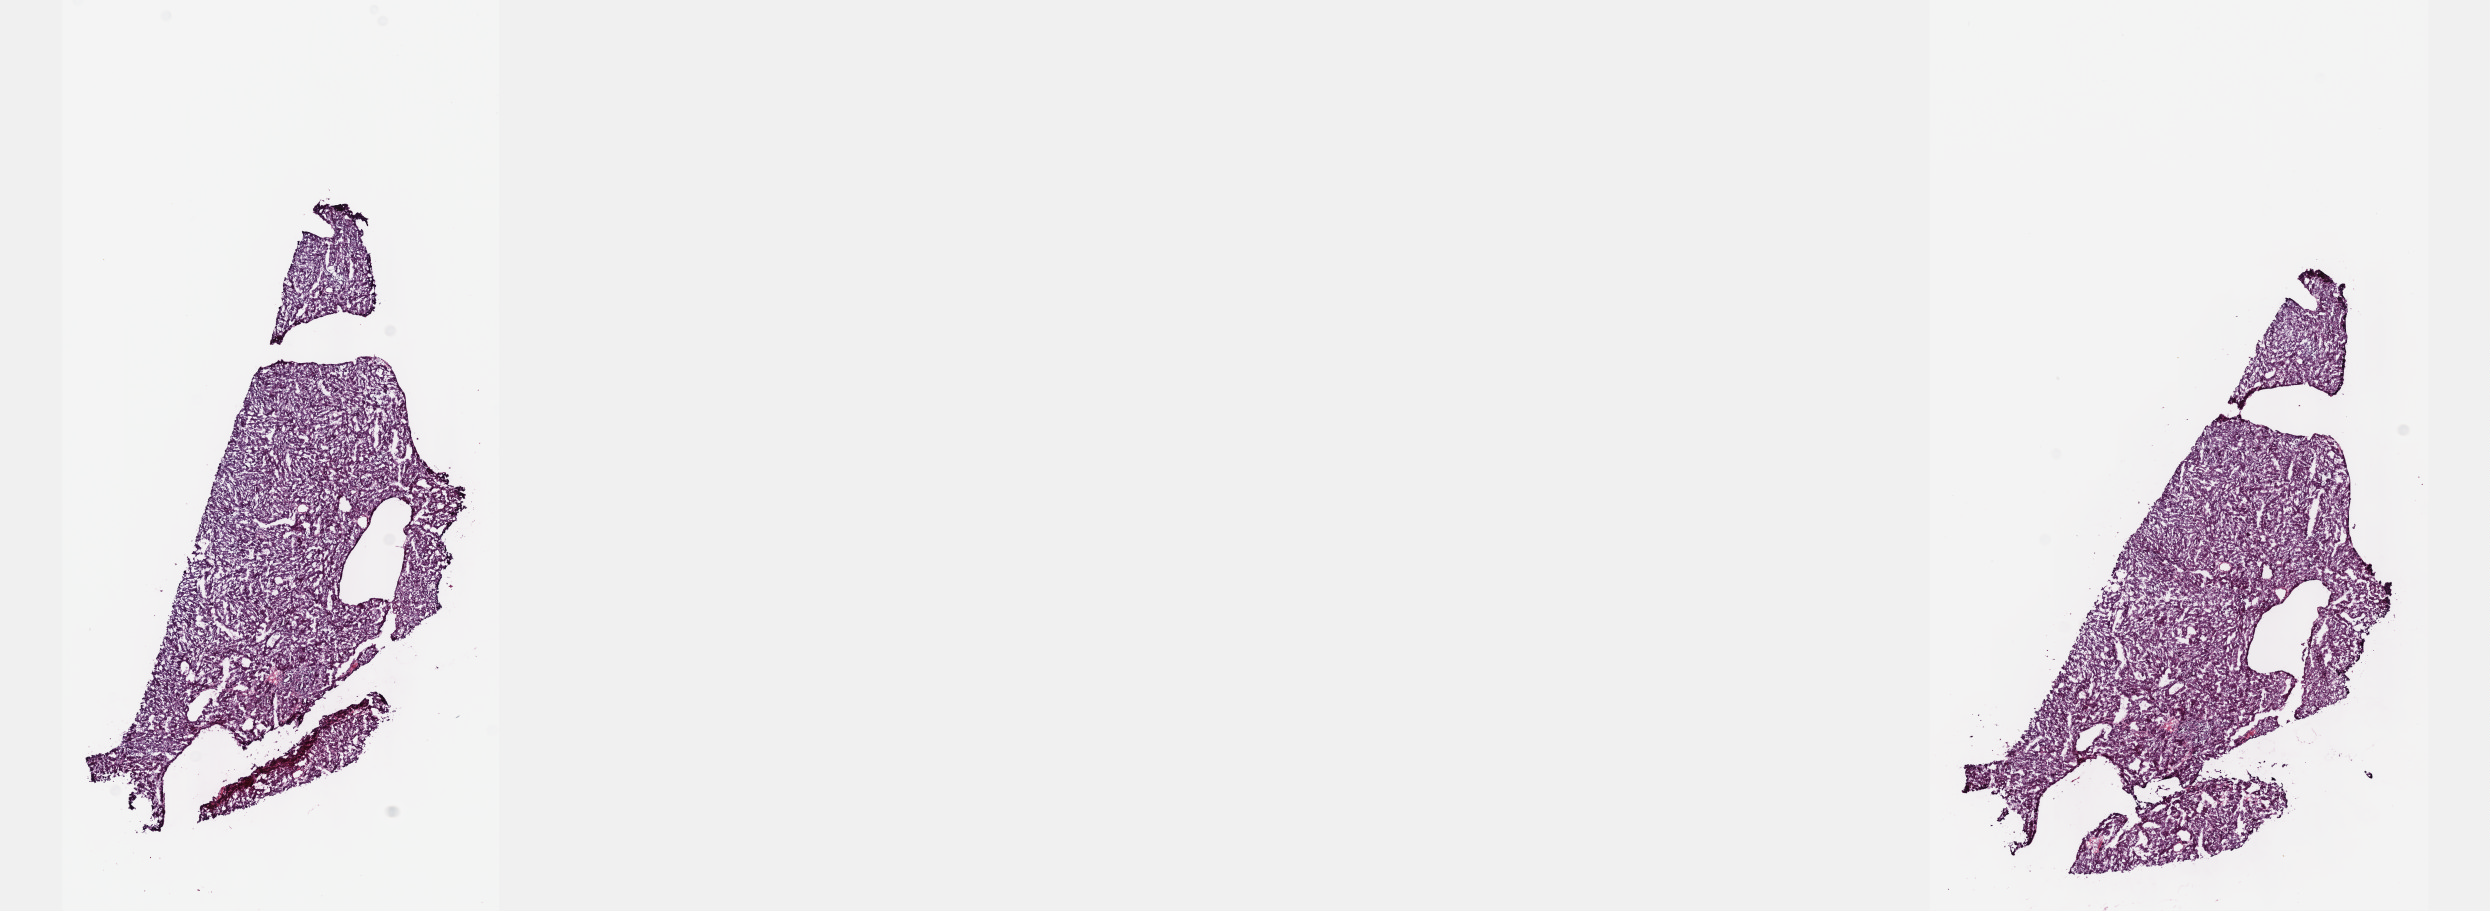
Digitized H&E tissue section (whole slide), whole scanned area (about 20.1 x 7.4 mm, from a 40x scan) shown as a low-resolution overview, frozen section, sample: primary tumour, liver. Patient: male, age at initial diagnosis 31 years. Histologic grade: G1 (well differentiated). Composition of this section per pathologist review: tumour cells 80%, tumour nuclei 80%, normal cells 0%, stromal cells 20%, necrosis 0%. Inflammatory infiltration, as recorded: lymphocyte infiltration 3%, monocyte infiltration 1%, neutrophil infiltration 1%.
* histologic diagnosis: Hepatocellular carcinoma, NOS
* AJCC pathologic stage: I (7th edition)